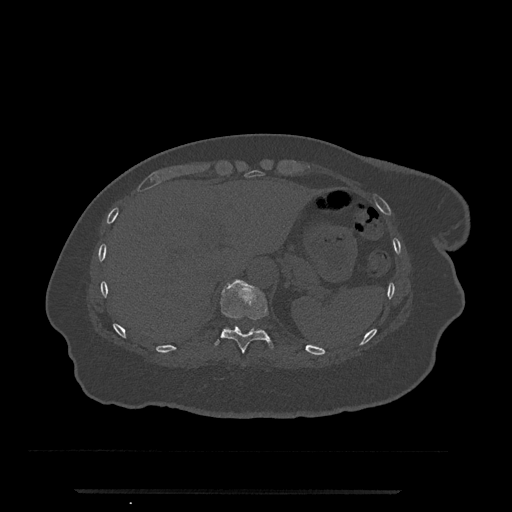
CT including the spine, one axial slice. Position 275 of 797 along the scan axis. 120 kVp. Bone window (W 1800 / L 400 HU). 0.5 mm slice thickness. 512 × 512 image matrix, field of view 440 × 440 mm. Patient: female, 51 years. Case-level facts recorded for this patient, not image findings: primary cancer: neuro; vertebrae with lytic lesions (as recorded): T8.
Annotated regions visible in this slice (semi-automatic segmentation, software-assisted and operator-edited):
- T10 vertebra: bounding box (x1, y1, x2, y2) in pixels: (214, 279, 274, 353)